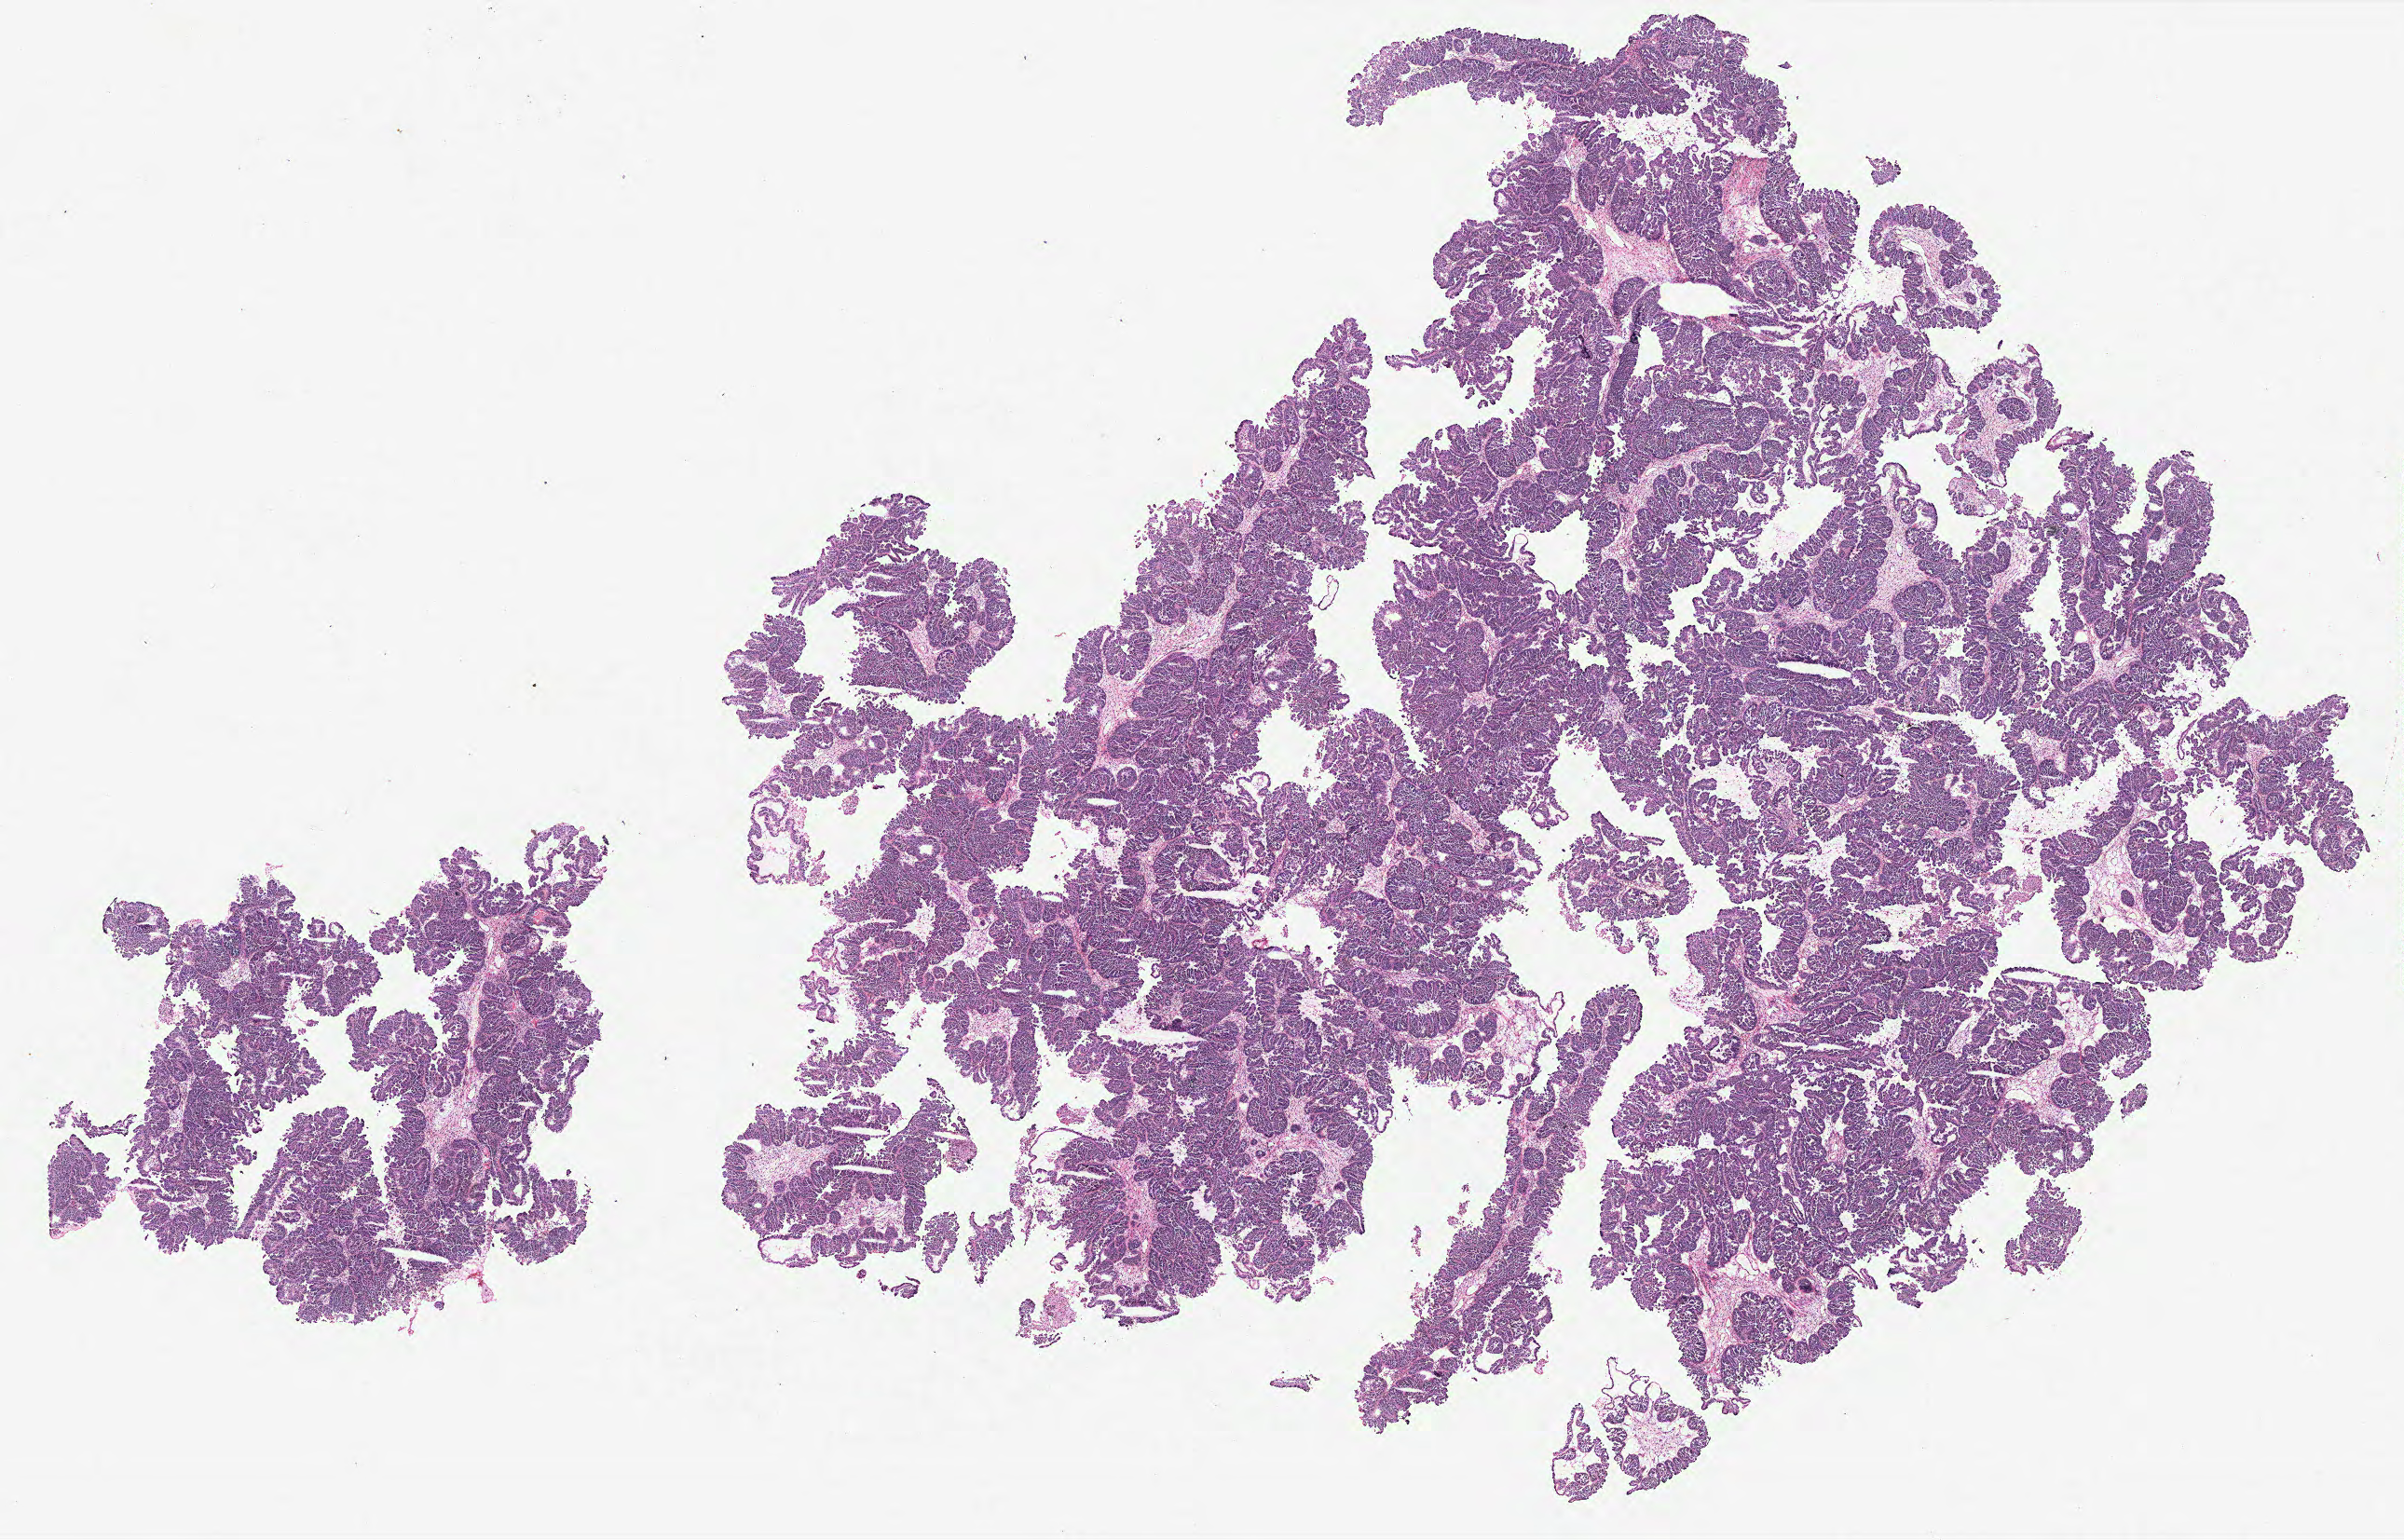
Hematoxylin and eosin (H&E) stained whole-slide image, shown as a low-resolution overview of the whole scanned area (about 20.6 x 13.2 mm), tumour tissue sample, ovary. Patient: female, age 48 years.
Histologic diagnosis: Serous adenocarcinoma, NOS (fallopian tube).